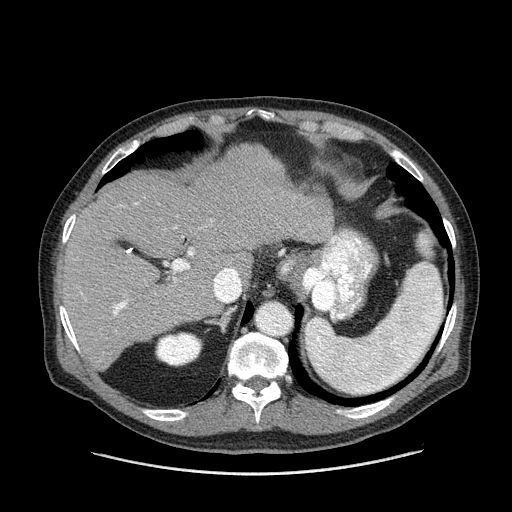
Contrast-enhanced abdominal CT (liver protocol), one axial slice. Slice 104 of 180 in the series (ordered by position). One of 2 acquisitions stored at this slice position. Soft-tissue window (W 400 / L 40 HU). 2.5 mm slice thickness. 512 × 512 image matrix, field of view 420 × 420 mm. Case-level facts recorded for this patient, not image findings: diagnosis: hepatocellular carcinoma (patient treated with transarterial chemoembolisation; whether this scan precedes or follows treatment is not stated here); TNM stage (as recorded): Stage-II; Child-Pugh class: A; tumour differentiation: well differentiated; tumour size: 2.8 cm.
Outlined on this slice (semi-automatic segmentation, software-assisted and operator-edited):
- liver parenchyma outside the tumour (the mass and vessels are separate outlines, so this box may not span the whole liver): bounding box [x1, y1, x2, y2] px = [60, 146, 334, 370]
- liver vessels: [72, 203, 212, 350]